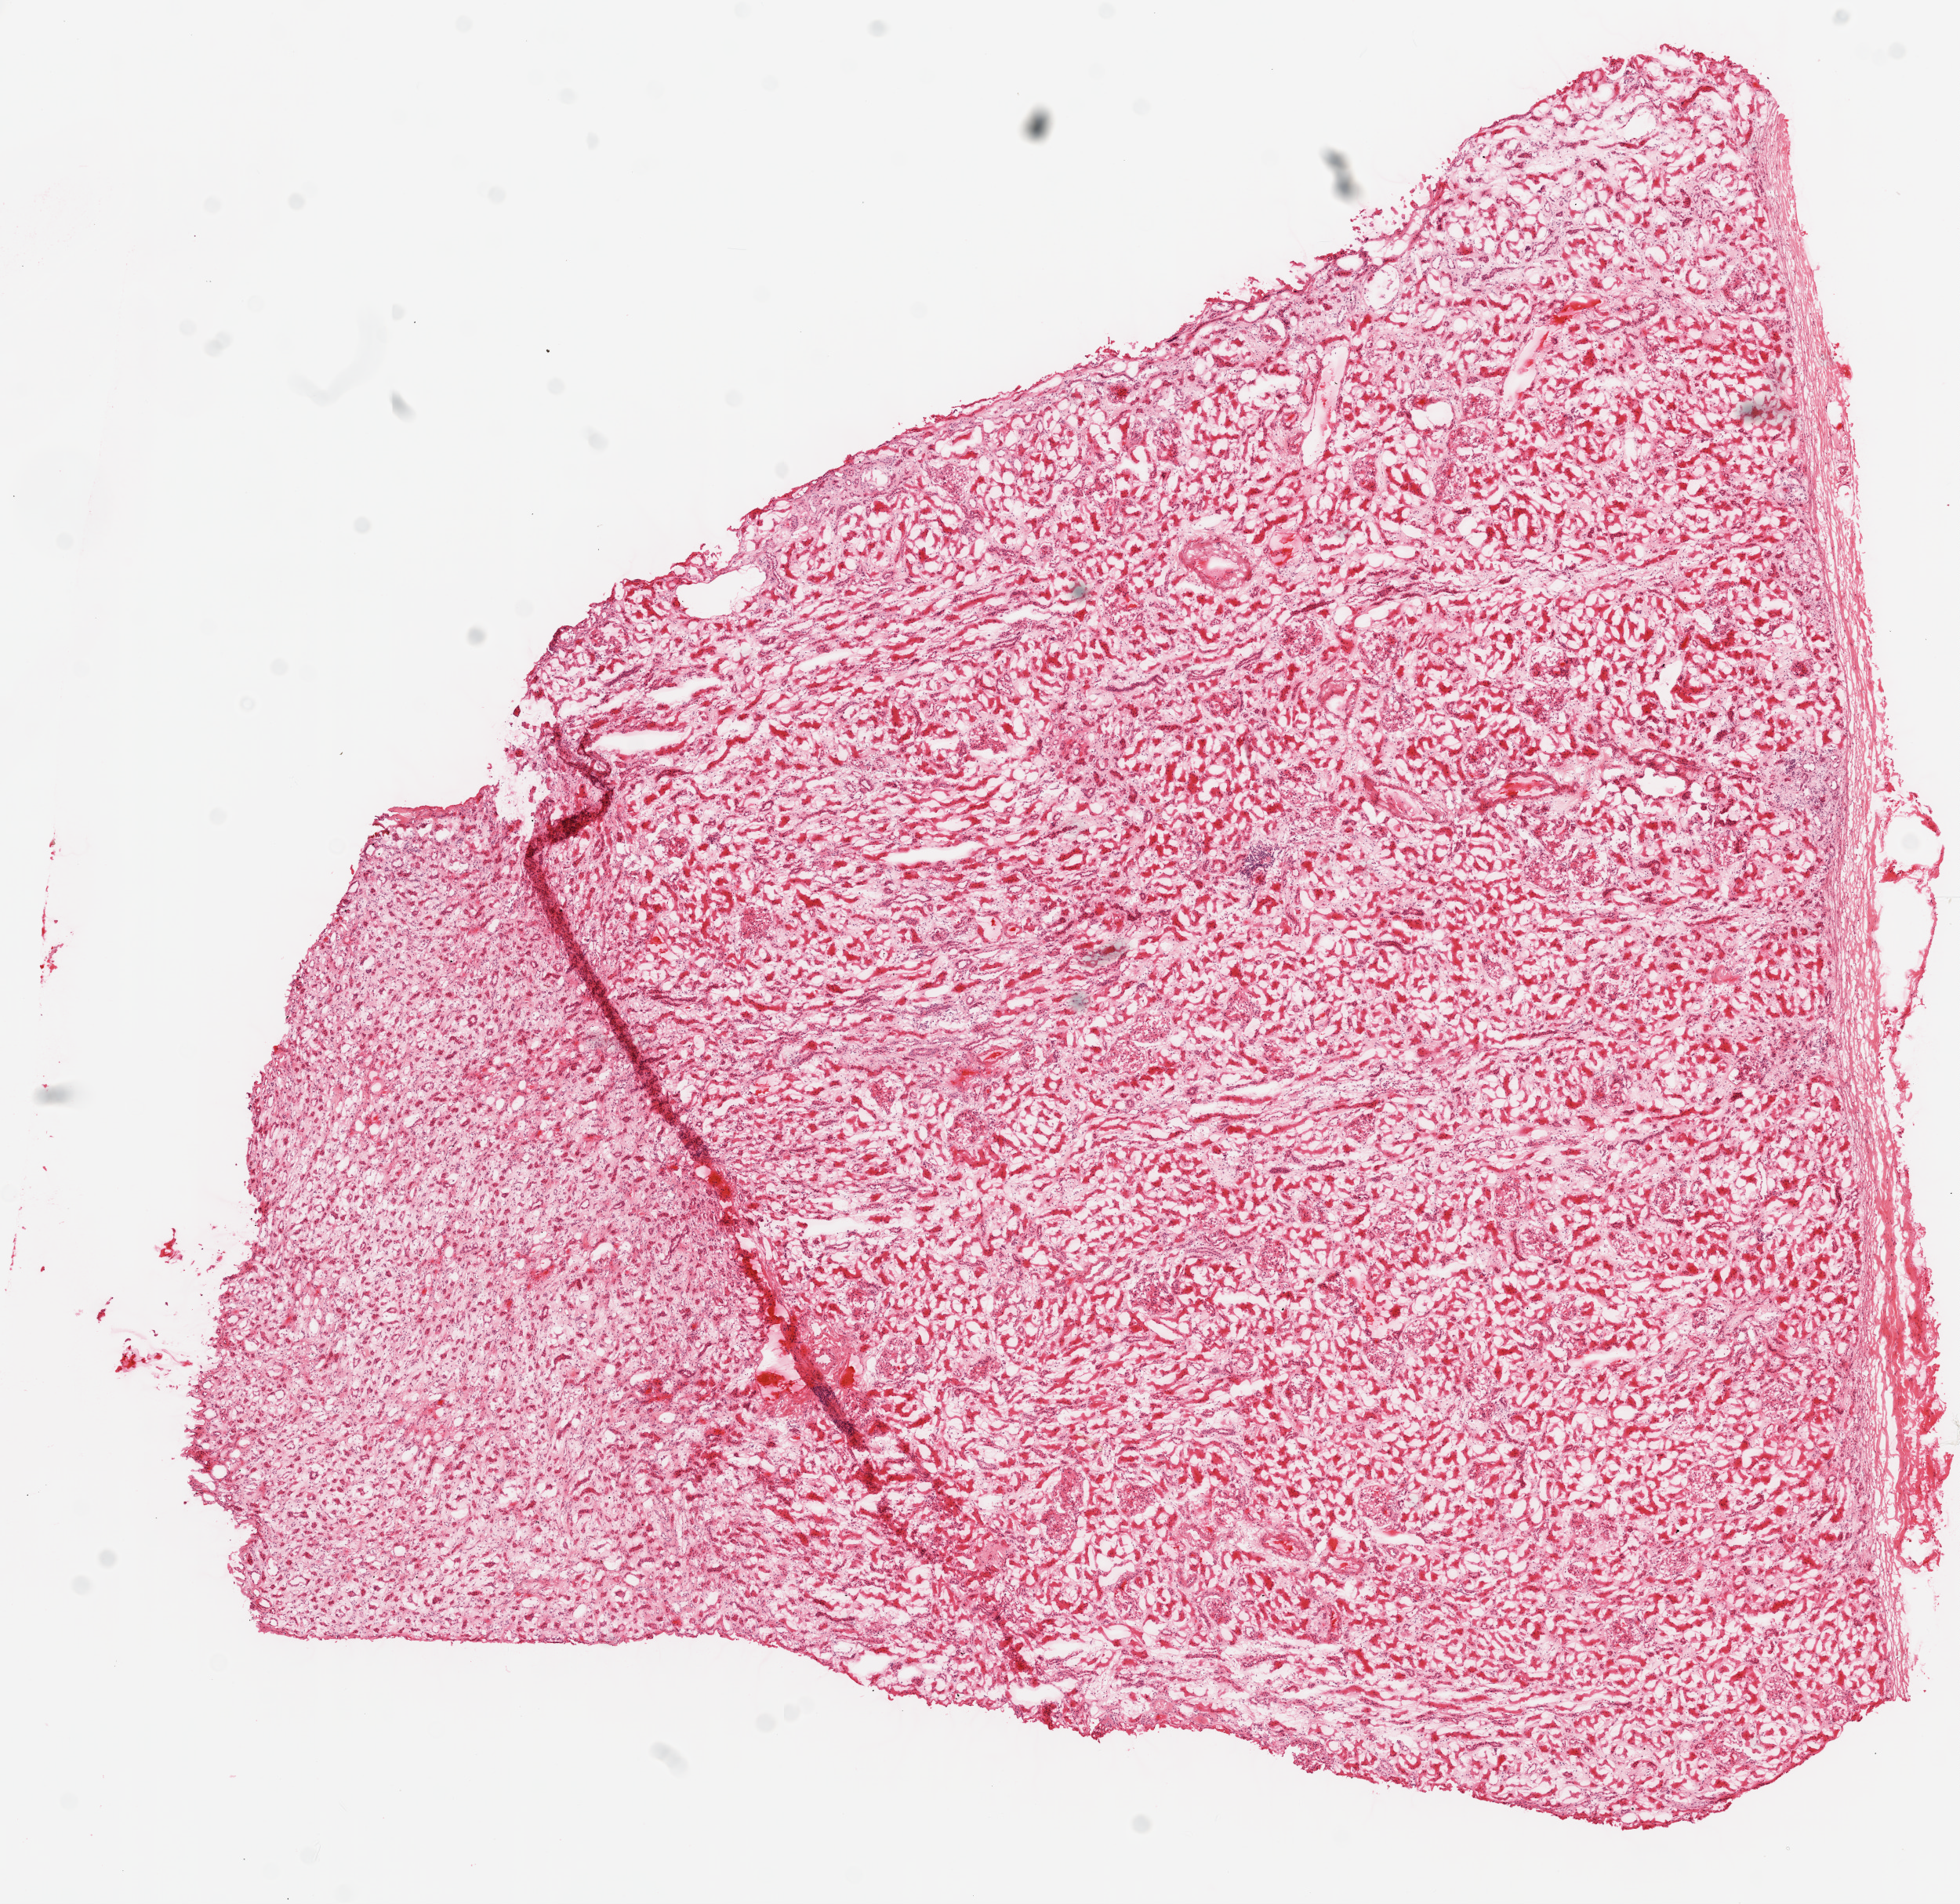
Whole-slide histology image, Hematoxylin and eosin (H&E) stained — shown as a low-resolution overview of the whole scanned area (about 10.0 x 9.7 mm). Frozen section from the top of the tissue portion. Sample: solid tissue normal (non-tumour tissue), kidney. Male patient; age at initial diagnosis 55 years.
This section: solid tissue normal sample (biorepository sample class). Patient diagnosis: Clear cell adenocarcinoma, NOS.